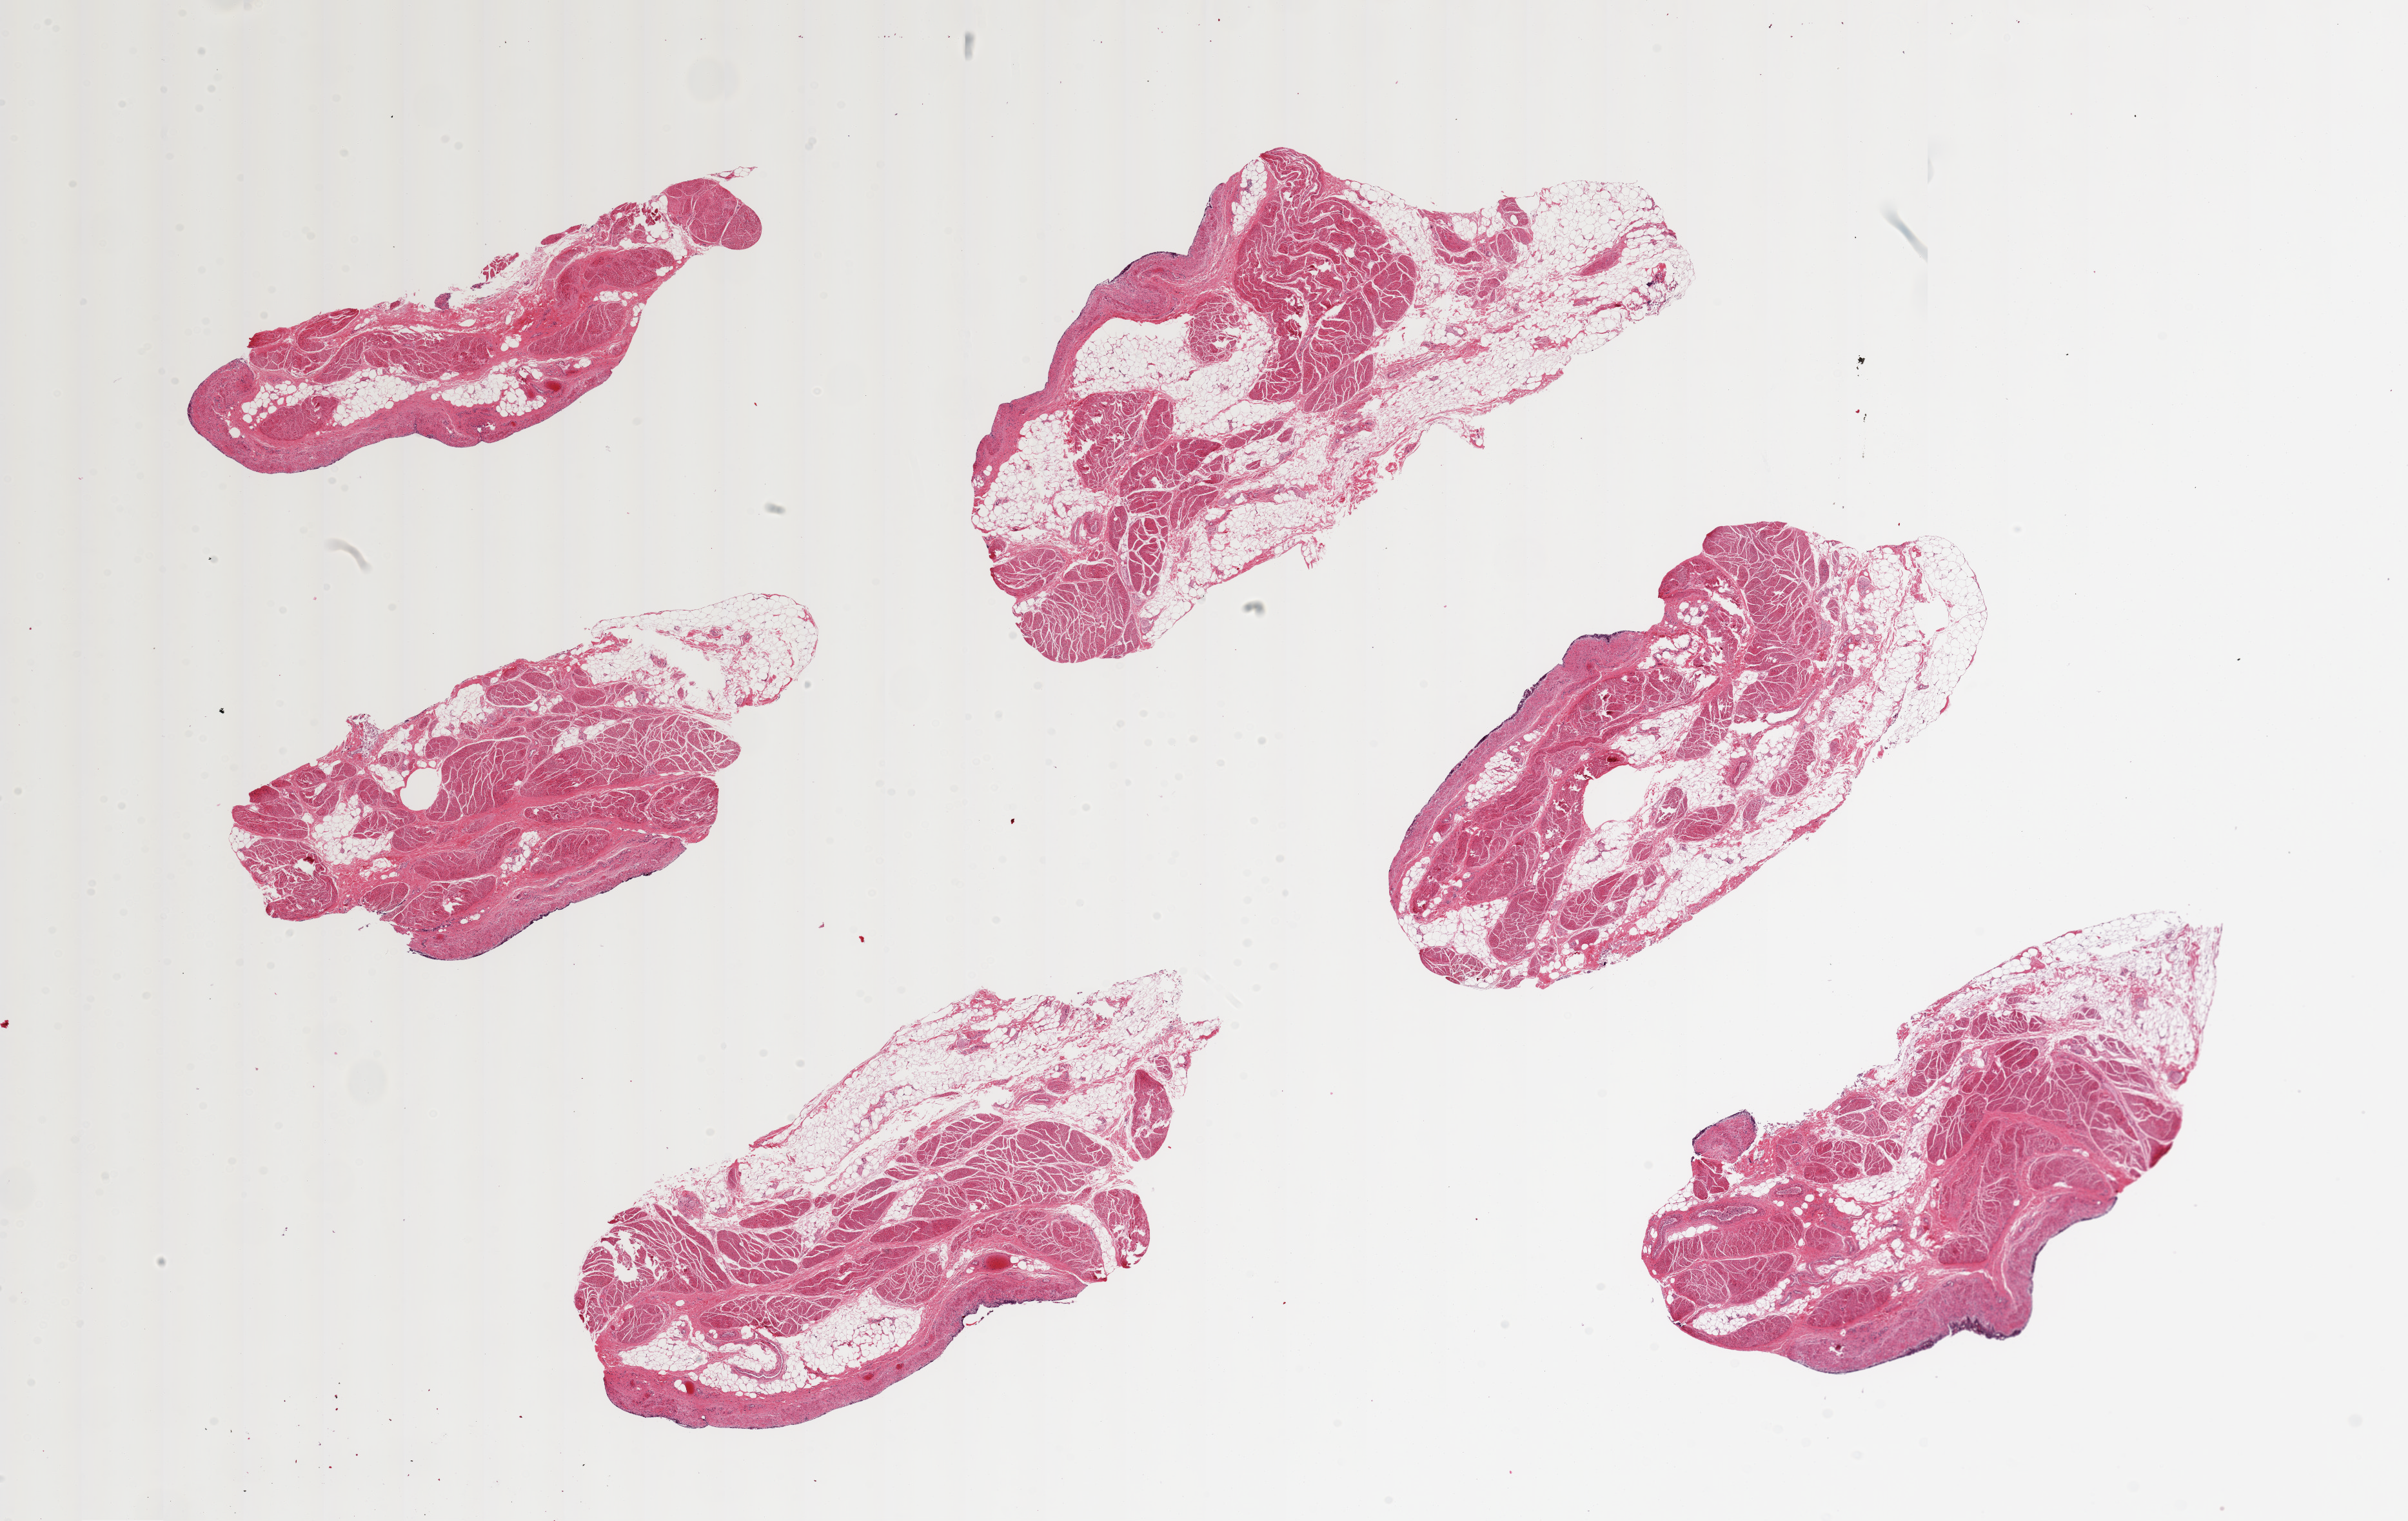
Whole-slide image, hematoxylin and eosin (H&E) stain — a low-resolution overview of the entire scanned area, about 29.5 x 18.7 mm. PAXgene-fixed paraffin-embedded (PFPE) section. Section of urinary bladder (target tissue). Donor tissue sample. Donor: female.
Review note (as recorded): 6 ~8 x 4mm pieces, urothelium 95% sloughed. Wall is ~50% fat/50%detrussor muscle.